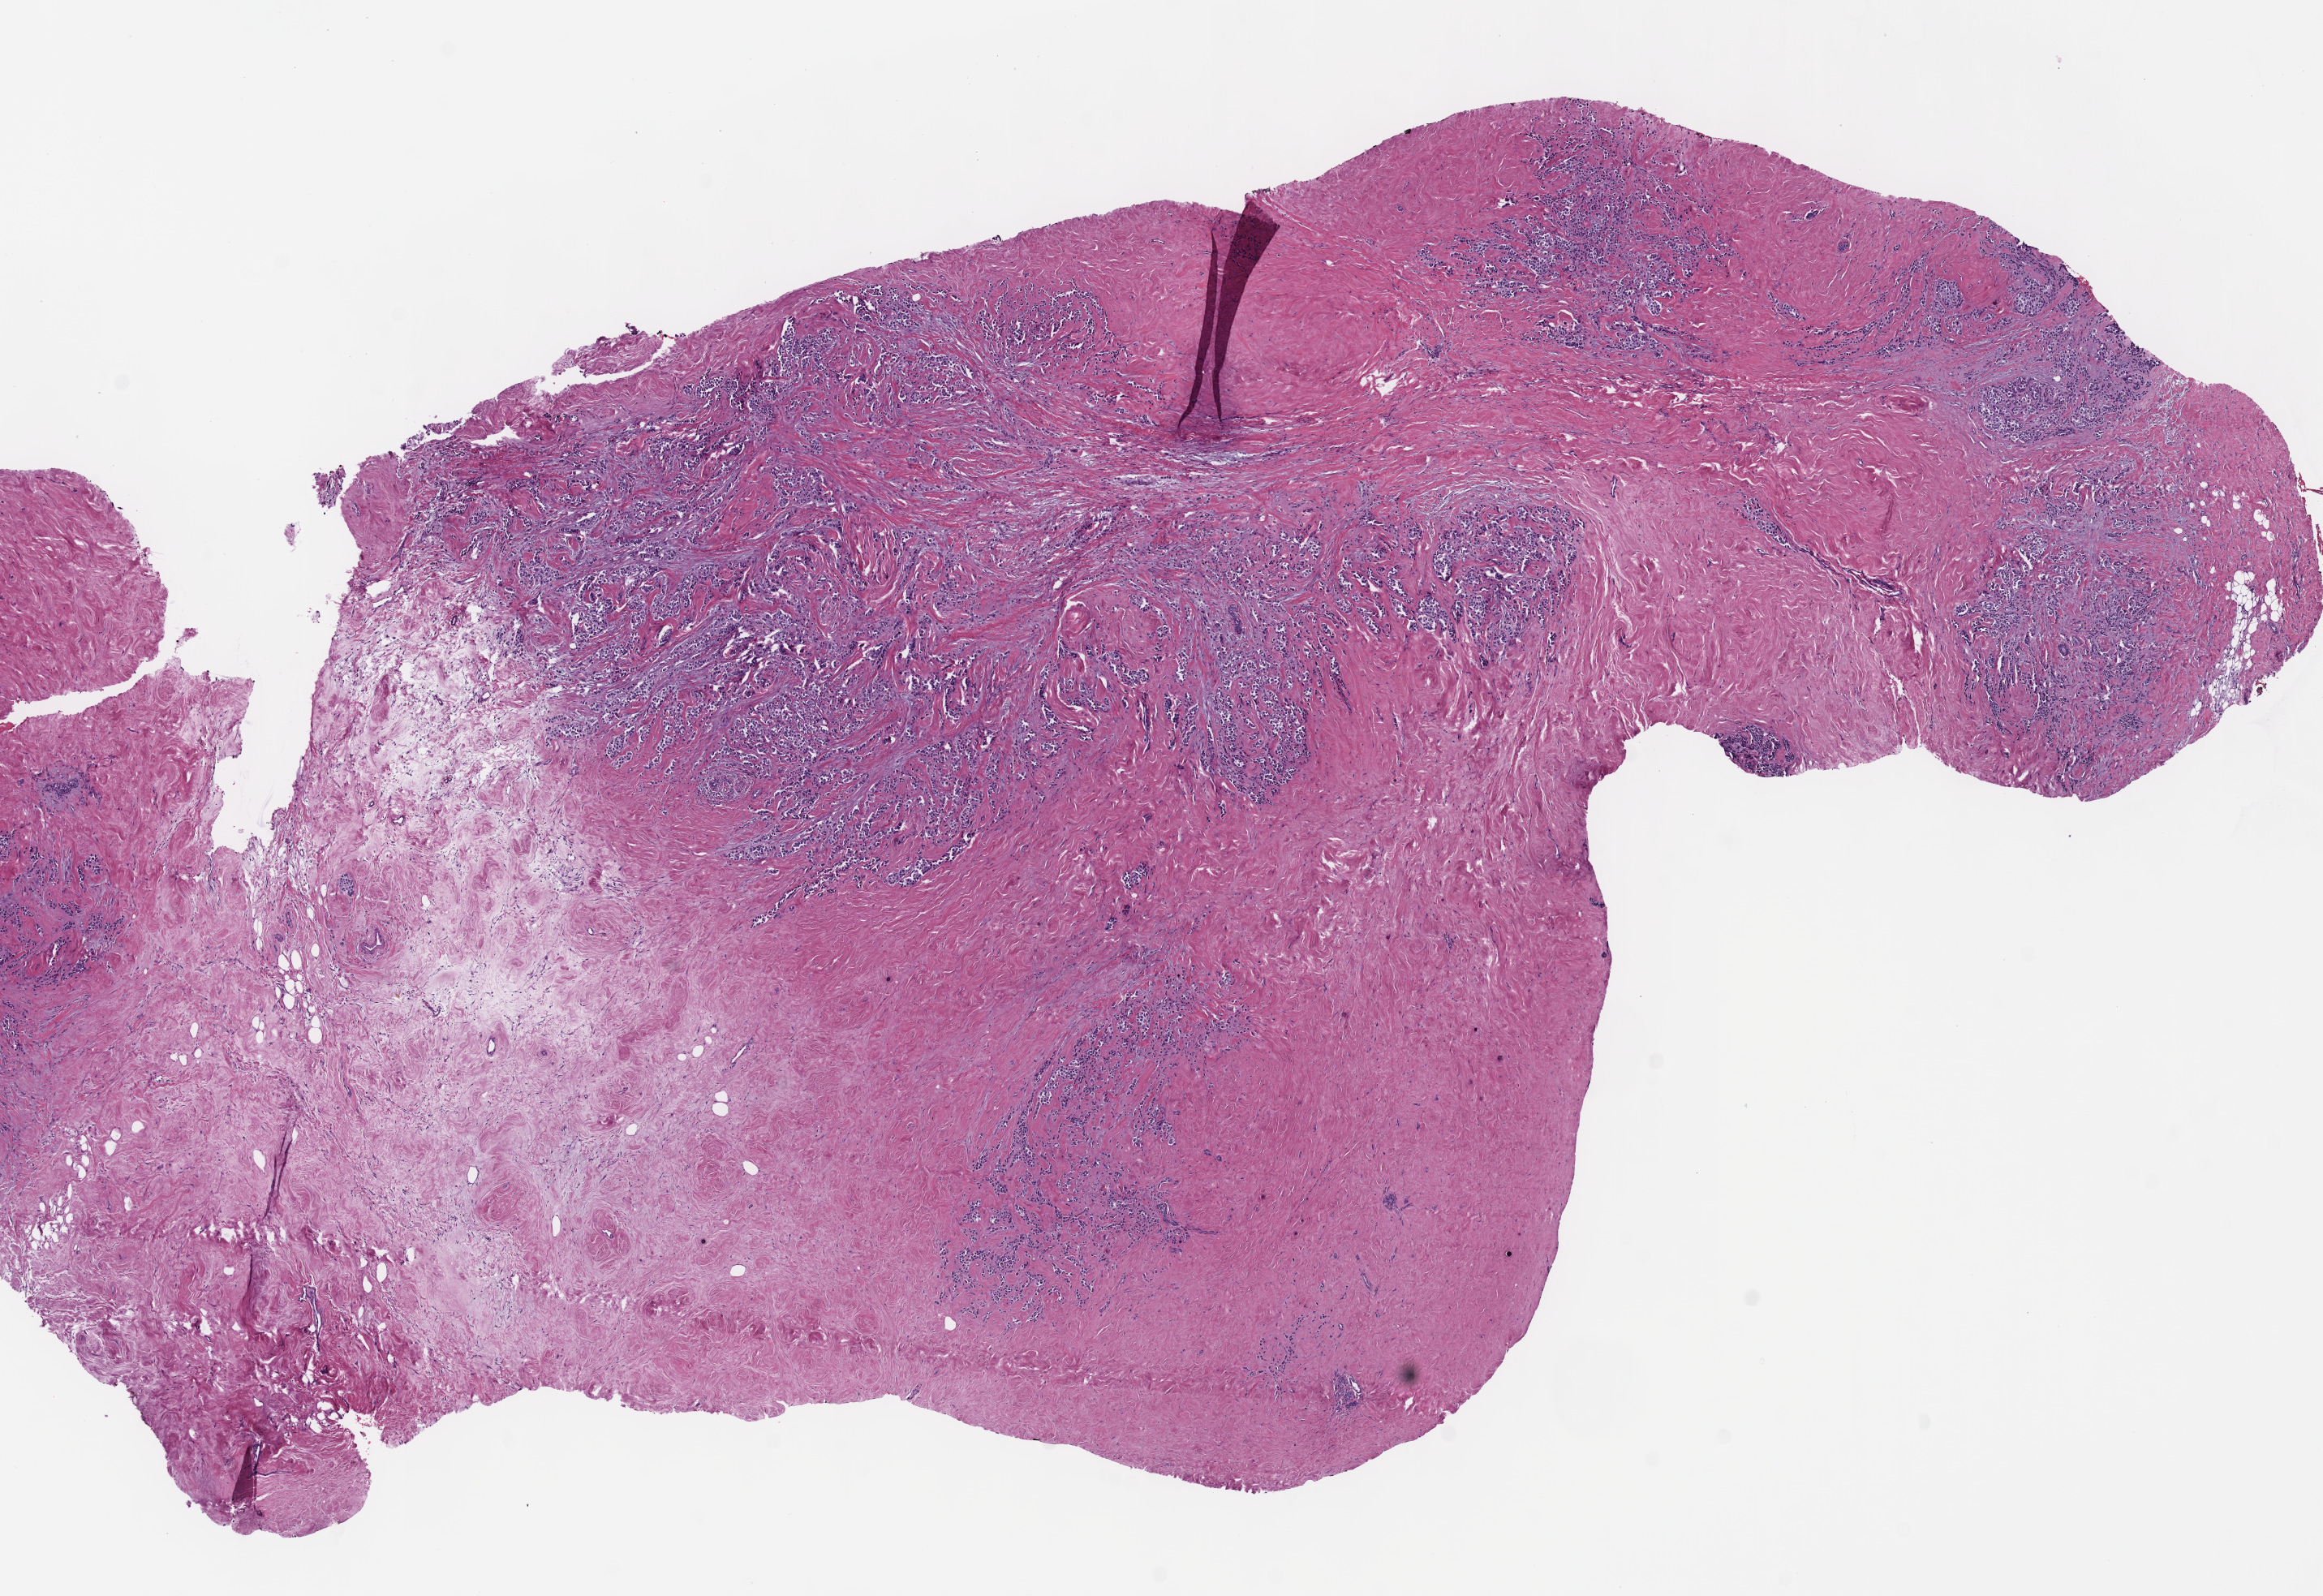
Digitized H&E-stained tissue section (whole slide) — a low-resolution overview of the entire scanned area, about 11.3 x 7.7 mm (from a 40x scan). Formalin-fixed paraffin-embedded (FFPE) diagnostic section. Primary tumour sample from the breast. Patient: female, age at initial diagnosis 79 years.
Histologic diagnosis: Pleomorphic carcinoma. AJCC pathologic stage: IIIC (7th edition). TNM: T3 N3 M0. Lymph nodes positive (case pathology): 12 of 12 examined. Laterality: right.